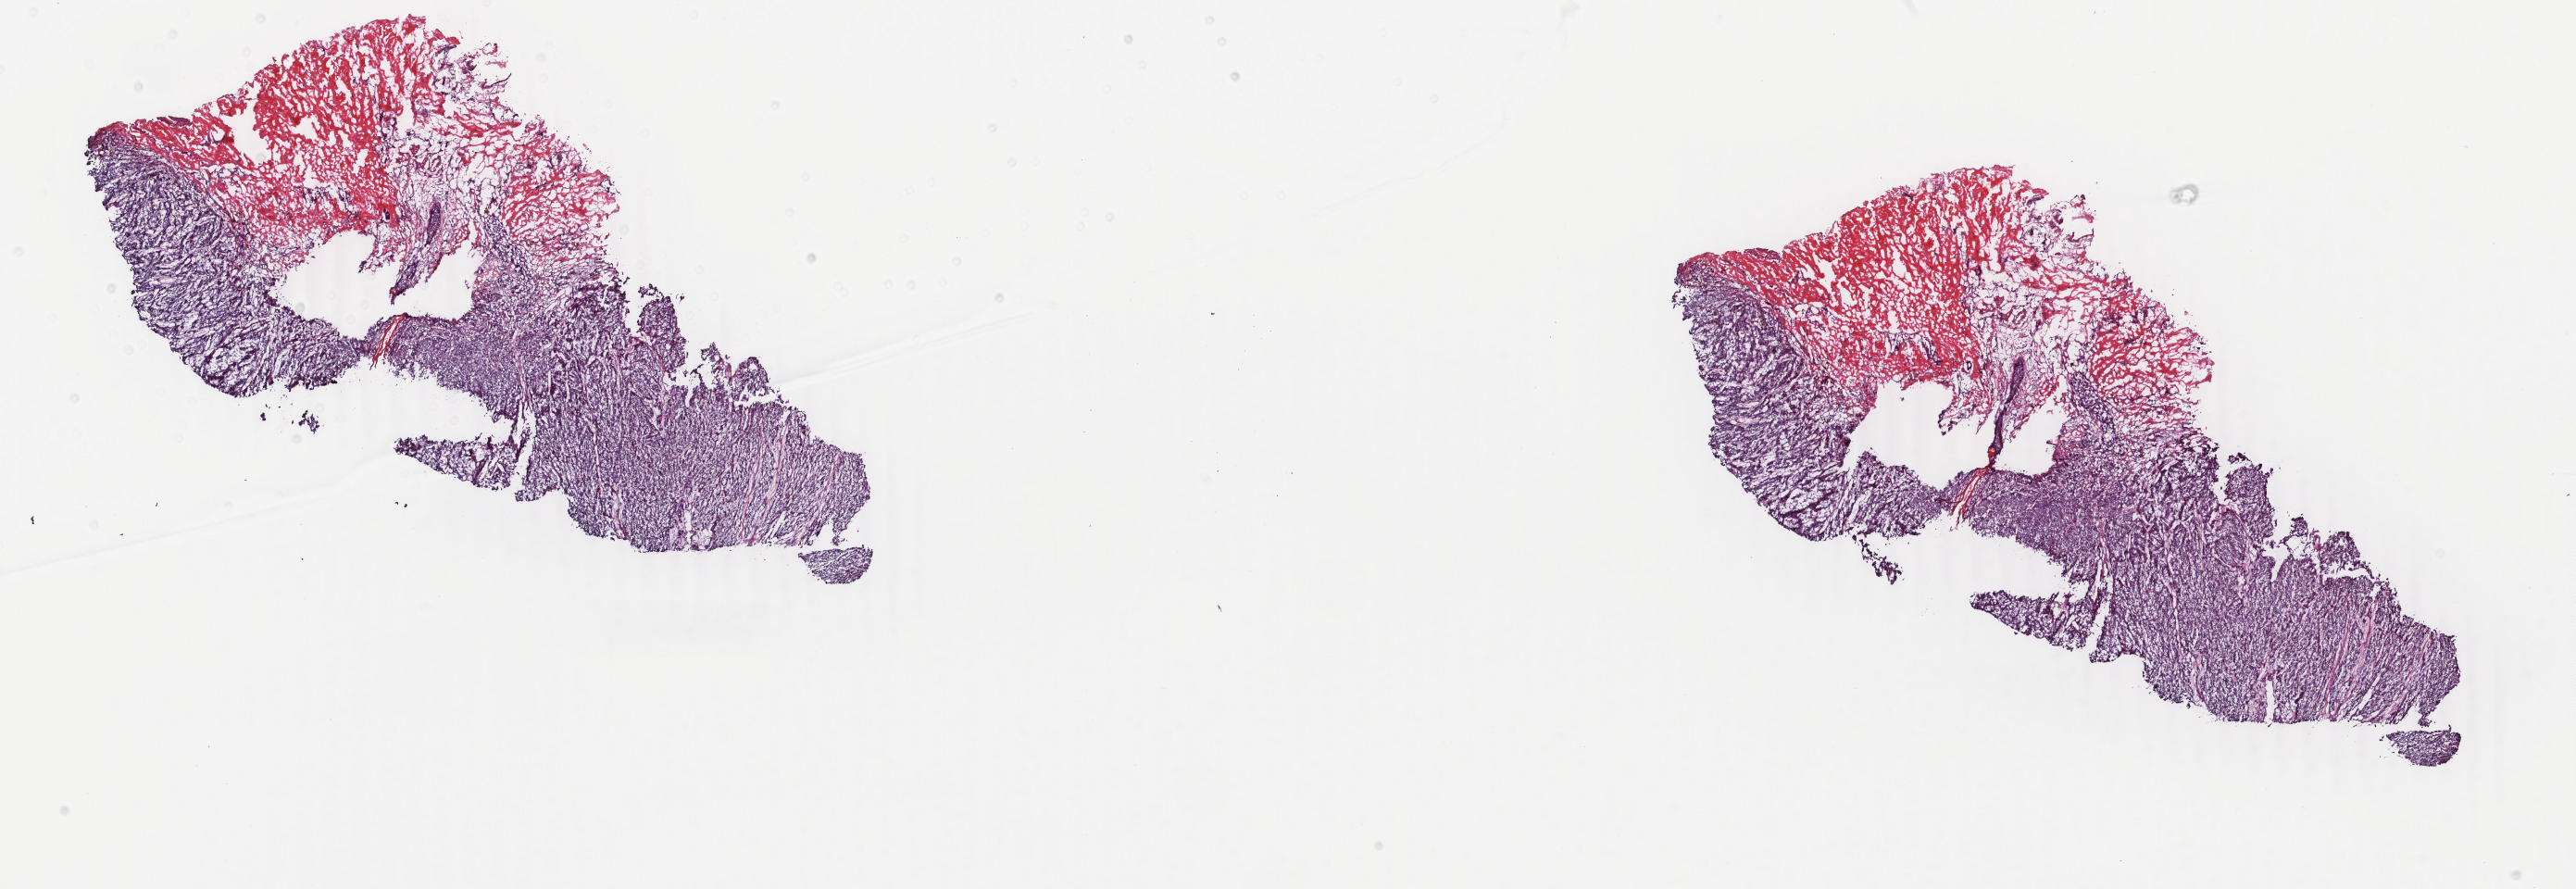
H&E whole-slide image — shown as a low-resolution overview of the whole scanned area (about 22.1 x 7.6 mm, acquisition: 40x scan), frozen section from the top of the tissue portion, skin, primary tumour sample. Patient: female, age at initial diagnosis 46 years. Pathologist review of this section (percent, as recorded): tumour cells 65%, tumour nuclei 95%, normal cells 35%, stromal cells 0%, necrosis 0%. Inflammatory infiltration, as recorded: lymphocyte infiltration 0%, monocyte infiltration 0%, neutrophil infiltration 0%.
AJCC pathologic stage: IIC (7th edition). Histologic diagnosis: Malignant melanoma, NOS. TNM: T4b N0 M0.